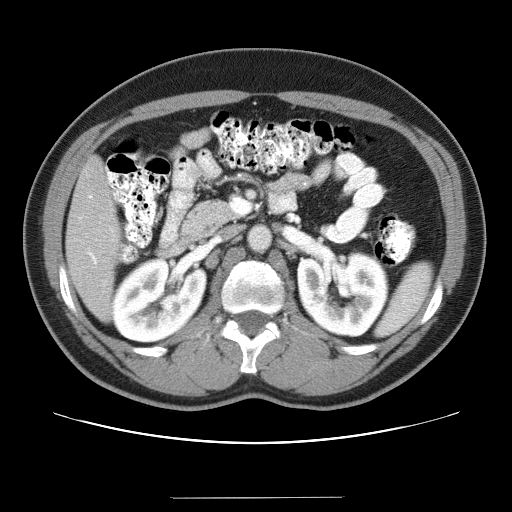
Contrast-enhanced abdominal CT (liver protocol), one axial slice; position 10 of 40 along the scan axis; reconstruction kernel STANDARD; 120 kVp; soft-tissue window (W 400 / L 40 HU); 512 × 512 image matrix. From the clinical record (not read from this slice): diagnosis: hepatocellular carcinoma (patient treated with transarterial chemoembolisation; whether this scan precedes or follows treatment is not stated here); TNM stage (as recorded): Stage-IVA; Child-Pugh class: B; tumour nodularity: multinodular.
Structures marked on this image (semi-automatically segmented with operator editing):
- liver parenchyma outside the tumour (the mass and vessels are separate outlines, so this box may not span the whole liver): bounding box (x1, y1, x2, y2) in pixels: (66, 156, 120, 320)
- liver vessels: (79, 195, 114, 264)